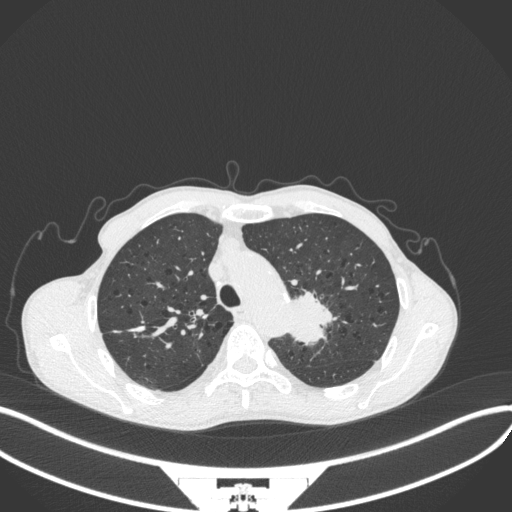
Chest CT, one axial slice; slice 316 of 394 in the series (ordered by position); reconstruction kernel B31f; 120 kVp; lung window (W 1500 / L -600 HU); 1 mm slice thickness; 512 × 512 image matrix, field of view 400 × 400 mm. Patient: male, 65 years. From the clinical record (not read from this slice): clinical TNM (as recorded): T2b N0 M0.
Structures marked on this image (bounding box drawn by a radiologist):
- lung tumour (recorded histology: adenocarcinoma): bounding box (x1, y1, x2, y2) in pixels: (283, 286, 337, 346)